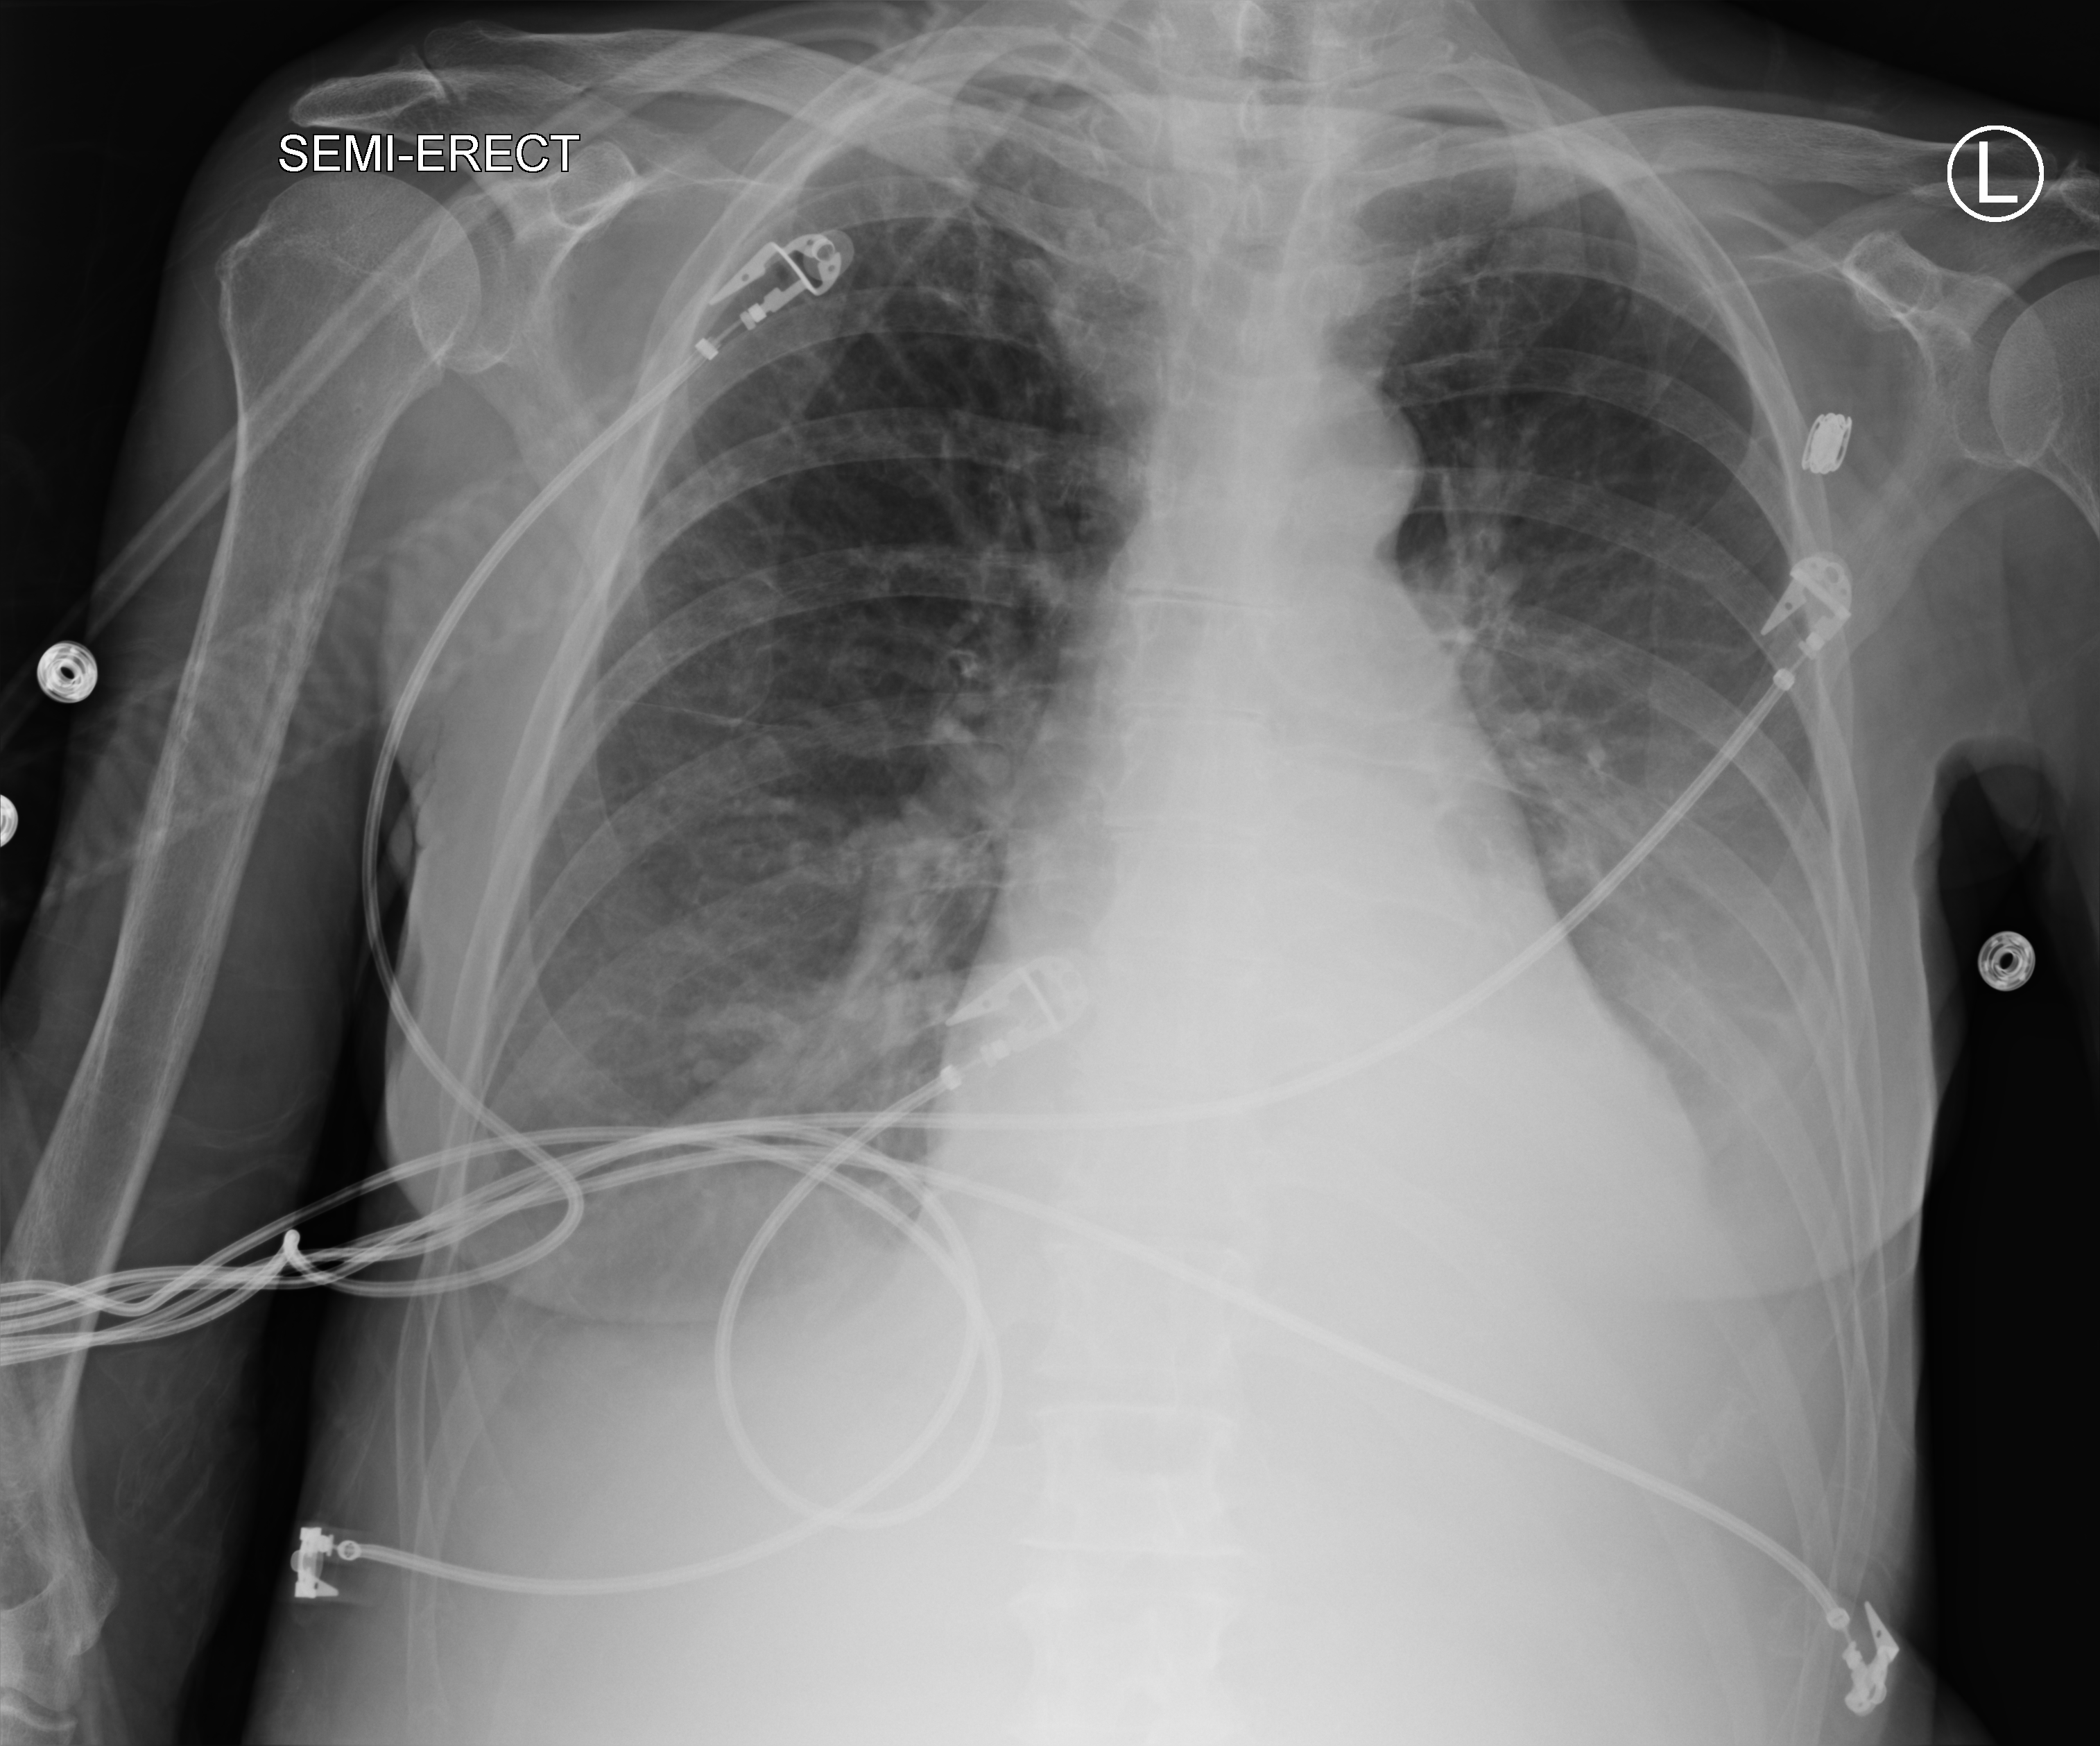
Portable chest radiograph, anteroposterior (AP) projection. Female patient hospitalised with COVID-19, age 60–74 years.
Admission-level facts for this patient (not findings on this image; timing relative to this image not recorded): length of hospital stay: 38 days; mechanically ventilated during this hospital stay: yes.